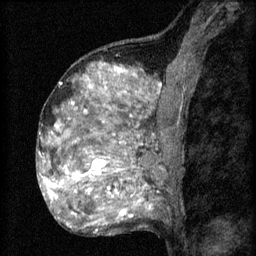
Breast MRI (dynamic contrast-enhanced), one sagittal slice. Position 38 of 60 along the scan axis. 3 images stored at this slice position (order not interpretable as contrast timing). 1.5 T. TE 4.2 ms, TR 8.2 ms. 2 mm slice thickness. 256 × 256 image matrix, field of view 180 × 180 mm. Patient: female, 48 years.
Annotated regions visible in this slice (semi-automatic segmentation, software-assisted and operator-edited):
- analysis volume of interest (the breast-tissue region the enhancement analysis was run in; not a lesion): box from (x=61, y=138) to (x=153, y=201) px
- tumour enhancement mask (voxels above the 70 % enhancement threshold inside the analysis volume of interest): (x=61, y=160)–(x=133, y=197)